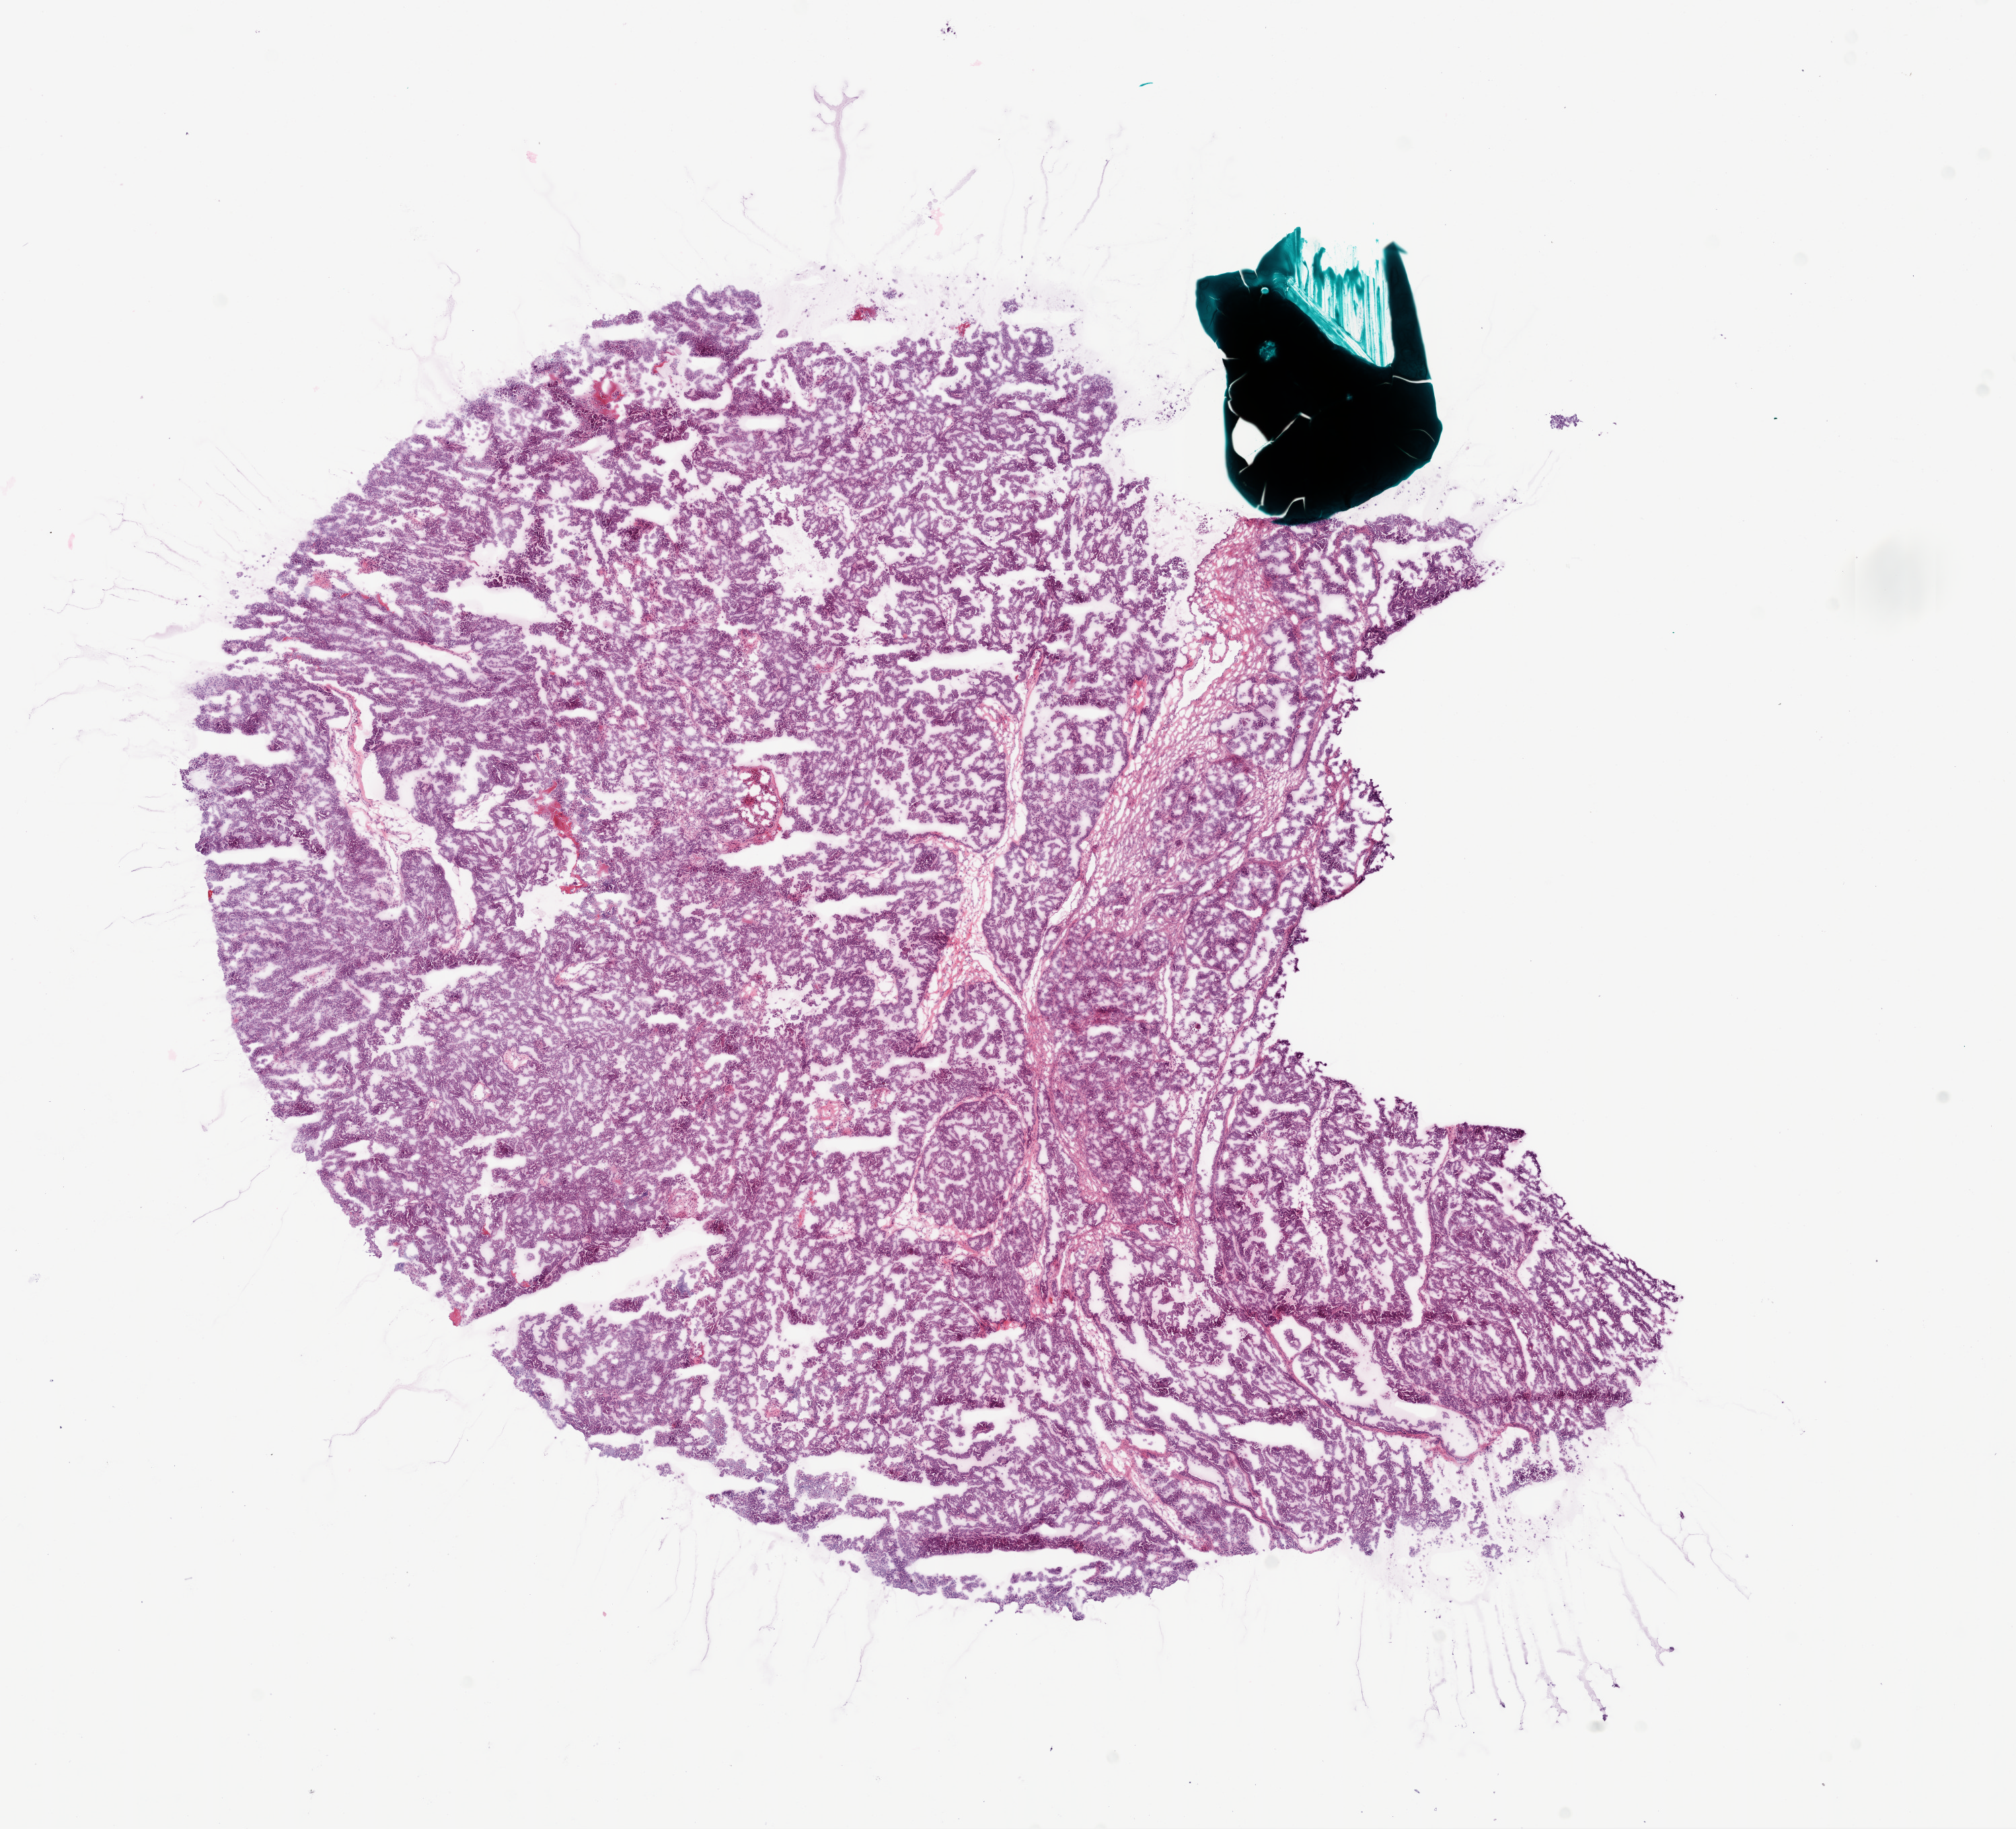
Whole-slide histology image, H&E — whole scanned area (about 12.1 x 11.0 mm) shown as a low-resolution overview, frozen section from the bottom of the tissue portion, primary tumour sample from the ovary. Female, age 44 years at initial diagnosis. Histologic grade: G3 (poorly differentiated). Pathologist review of this section (percent, as recorded): tumour cells 95%, tumour nuclei 98%, normal cells 0%, stromal cells 5%, necrosis 0%.
- diagnosis: Serous cystadenocarcinoma, NOS
- FIGO stage: IIIC
- laterality: bilateral